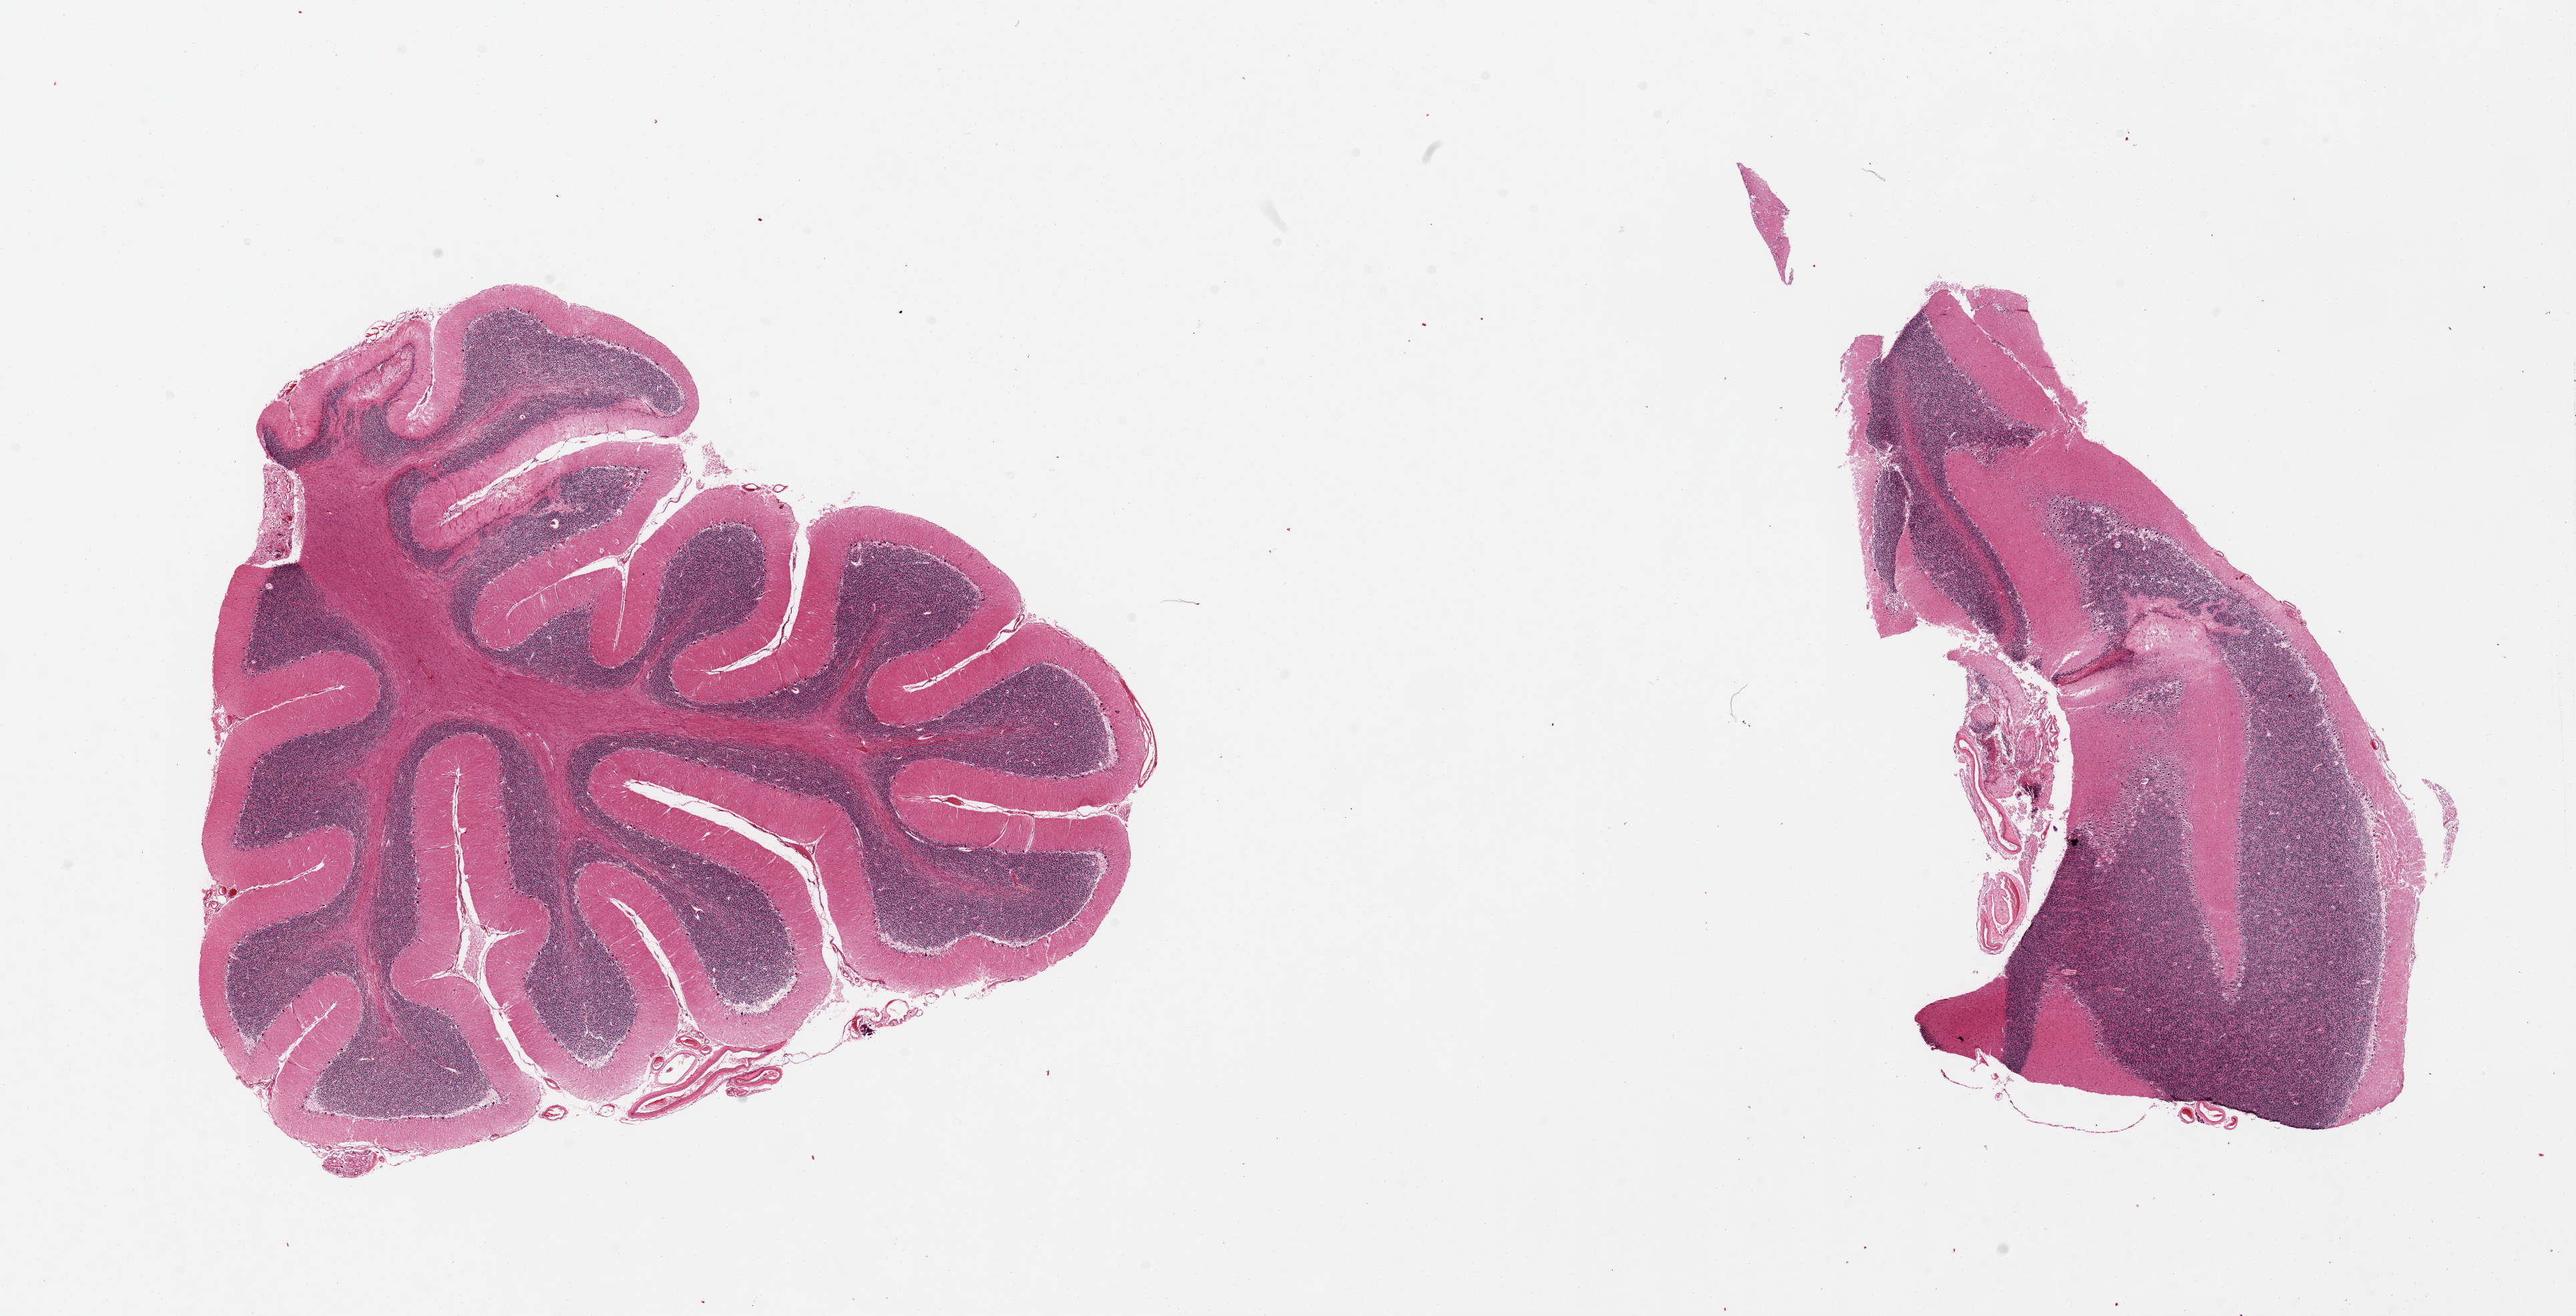
H&E whole-slide image, brightfield — shown as a low-resolution overview of the whole scanned area (about 30.5 x 15.6 mm, acquisition: 20x scan). PAXgene-fixed, paraffin-embedded tissue. Section of cerebellum (target tissue). Tissue donor sample. Donor: female.
* pathologist's review note for this sample: 2 pieces, moderate autolysis